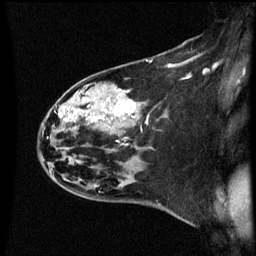
Breast MRI (dynamic contrast-enhanced), one sagittal slice. Slice 39 of 60 in the series (ordered by position). Dynamic contrast-enhanced series, image 2 of 3 at this slice position (ordered by acquisition). 1.5 T. TE 4.2 ms, TR 8.9 ms. 2 mm slice thickness. 256 × 256 image matrix, field of view 200 × 200 mm. Female patient, age 44 years. From the clinical record (not read from this slice): setting: breast cancer imaged before/during neoadjuvant chemotherapy; receptor status: HR-positive, HER2-negative.
Outlined on this slice (semi-automatic segmentation, software-assisted and operator-edited):
- analysis volume of interest (the breast-tissue region the enhancement analysis was run in; not a lesion): bounding box <43,78,153,189> (left, top, right, bottom; pixels)
- tumour enhancement mask (voxels above the 70 % enhancement threshold inside the analysis volume of interest): <91,106,135,121>